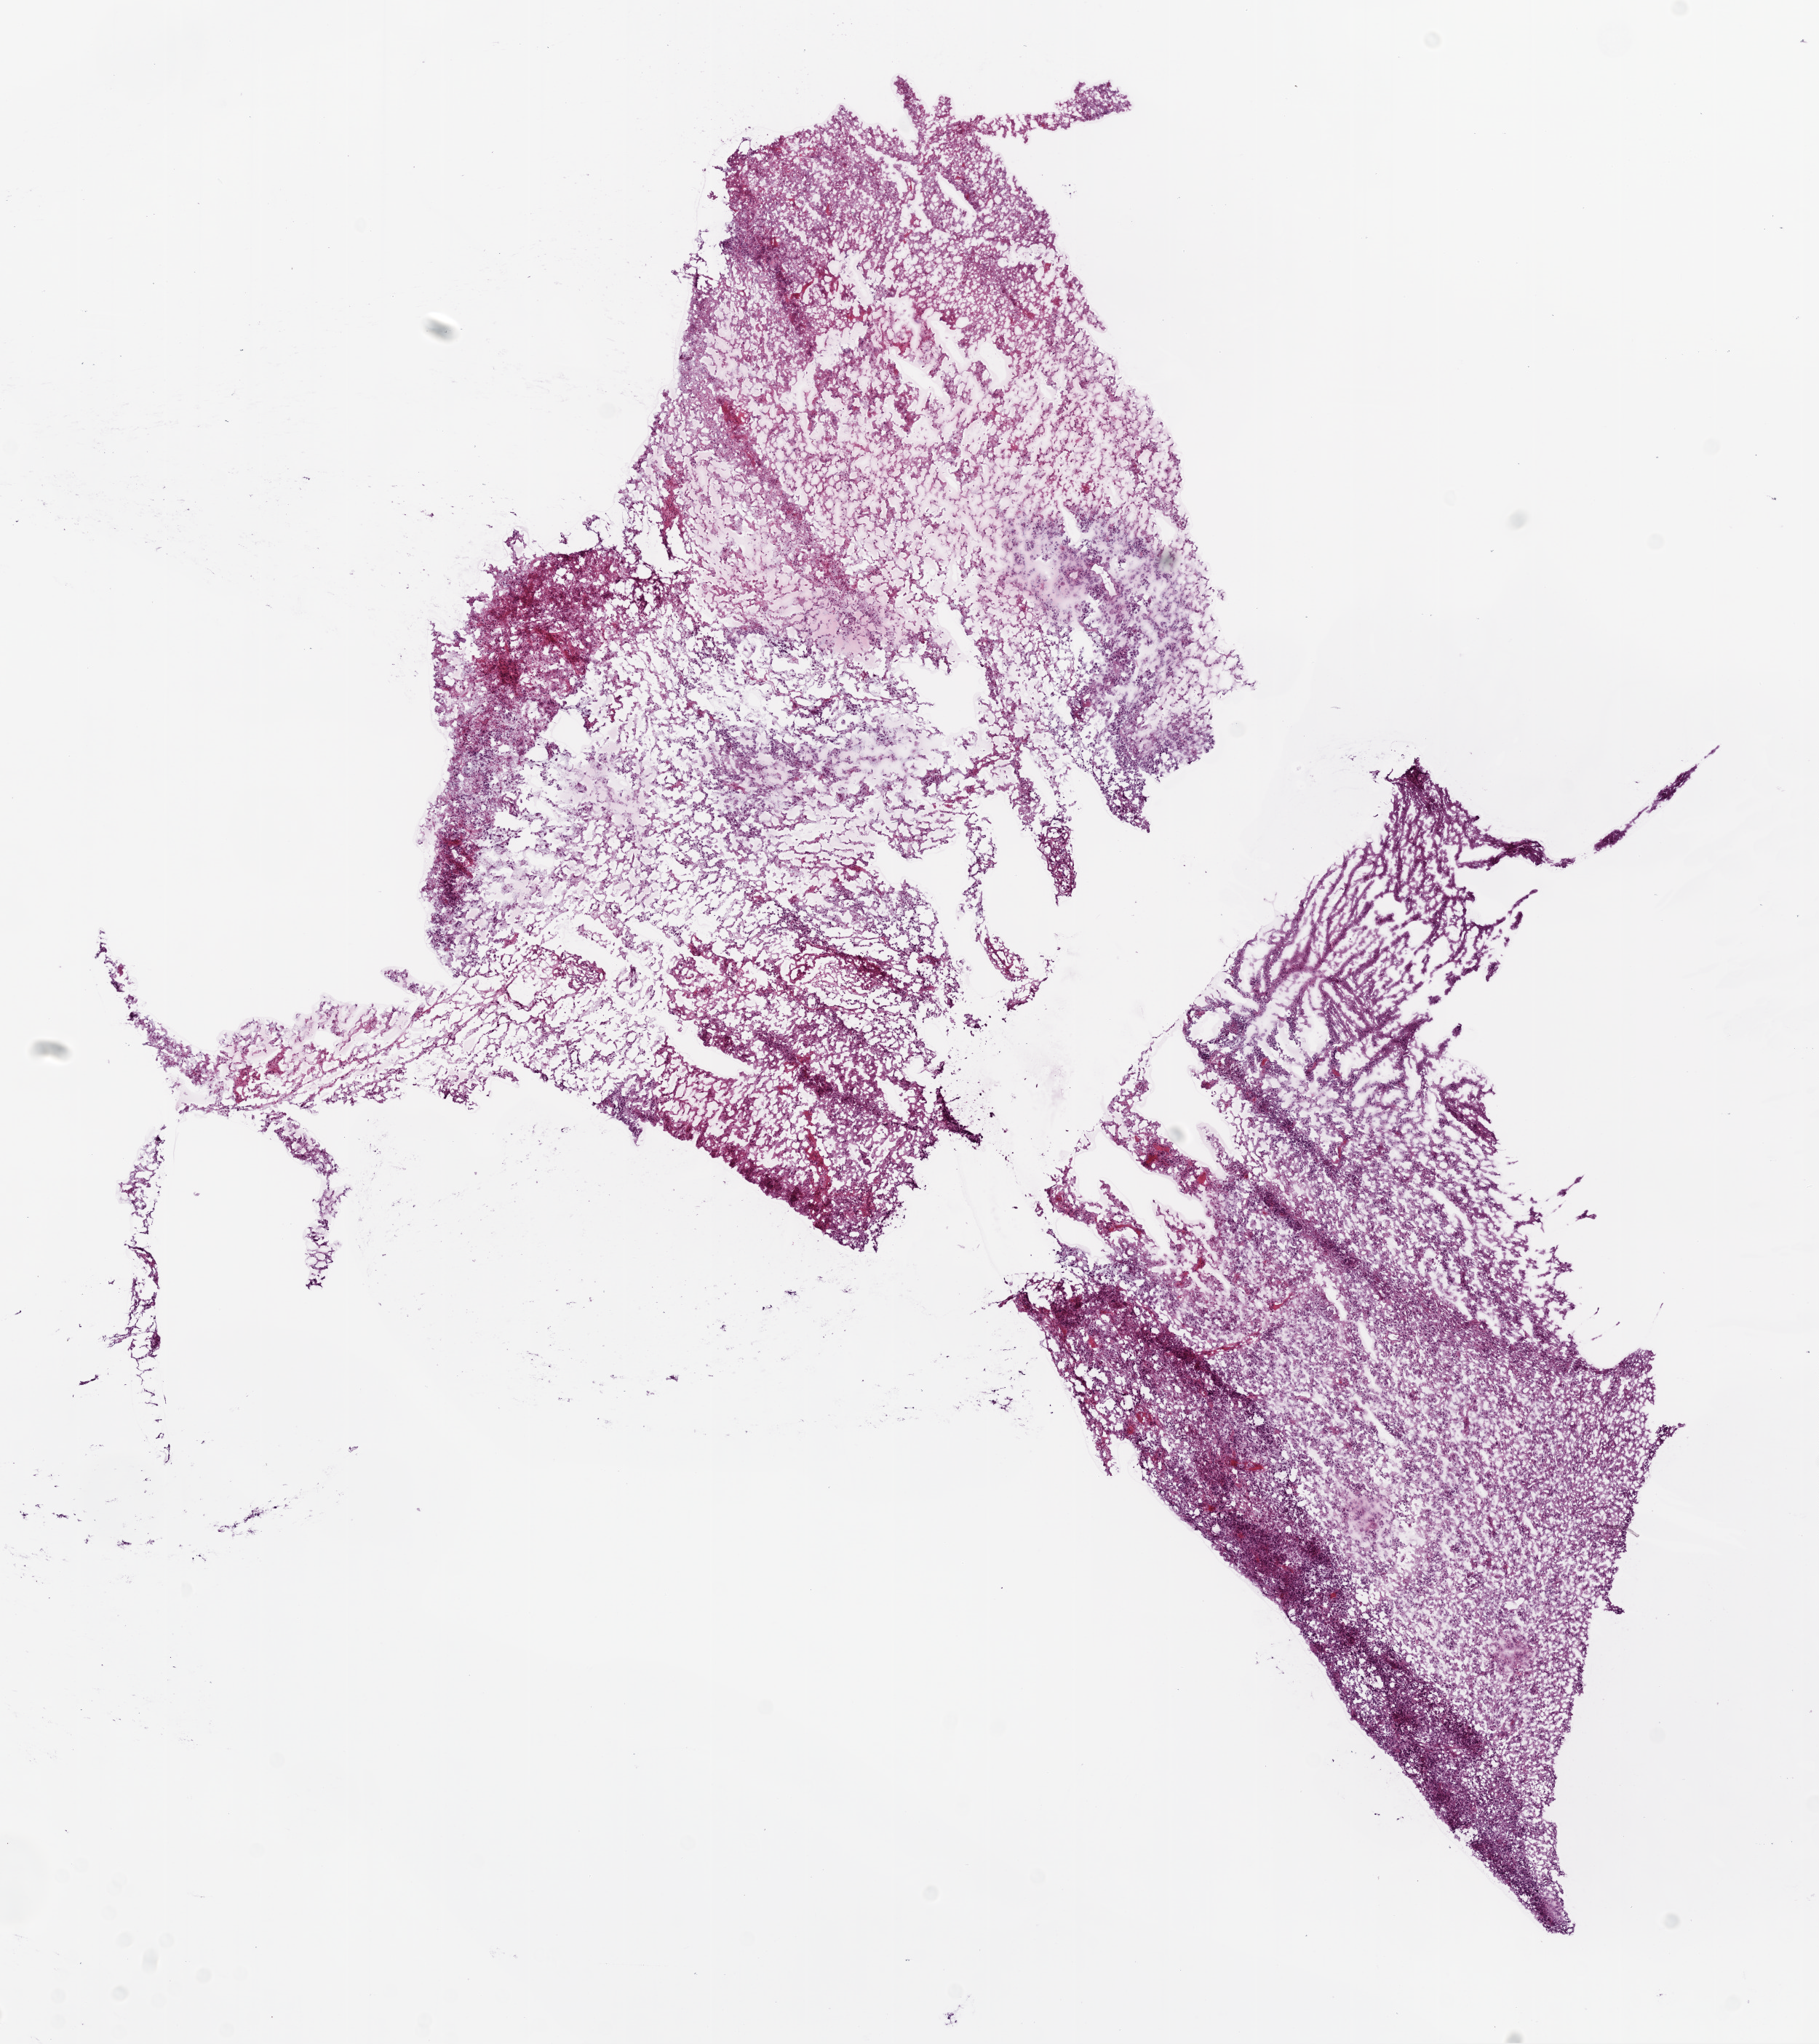
H&E-stained whole-slide image, whole scanned area (about 10.0 x 11.3 mm, slide scanned at 20x) shown as a low-resolution overview, frozen section, primary tumour sample from the brain. Patient: male, age at initial diagnosis 48 years. Composition of this section per pathologist review: tumour cells 80%, tumour nuclei 85%, normal cells 0%, stromal cells 5%, necrosis 15%.
* histologic diagnosis: Glioblastoma